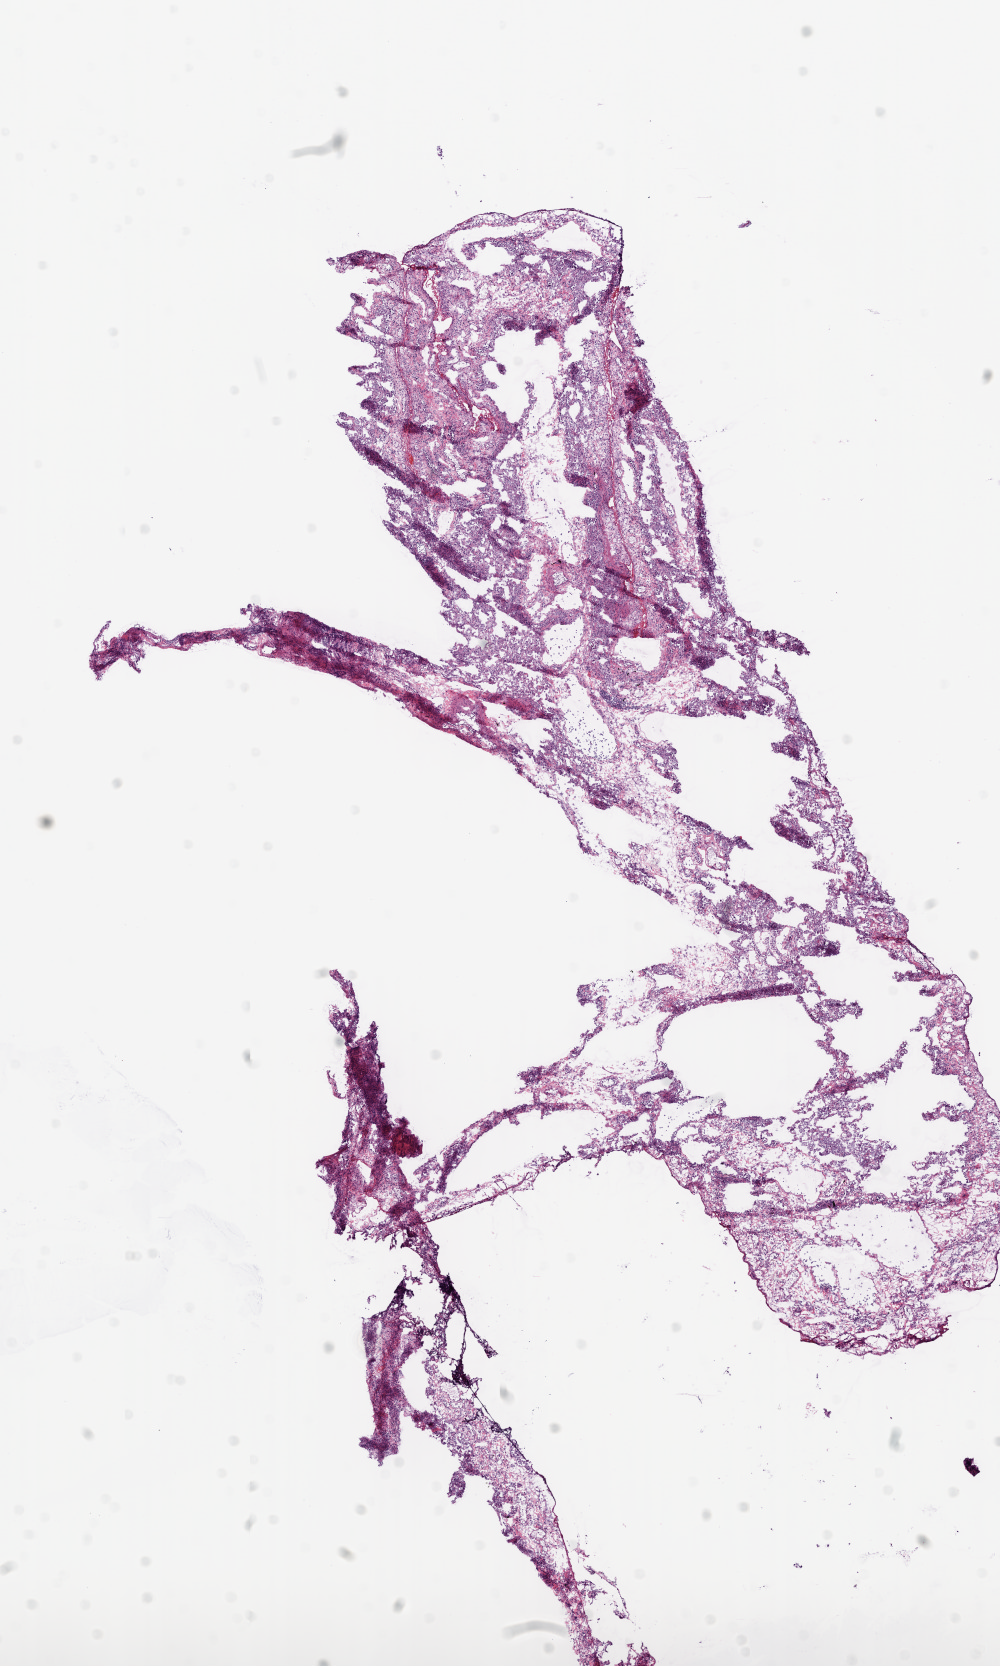
Whole-slide histology image, H&E — shown as a low-resolution overview of the whole scanned area (about 8.0 x 13.4 mm), frozen section, solid tissue normal (non-tumour tissue) sample from the lung. Male, age 67 years at initial diagnosis.
This section: solid tissue normal (non-tumour) sample from the same patient. Patient diagnosis: Squamous cell carcinoma, NOS (lower lobe, lung).